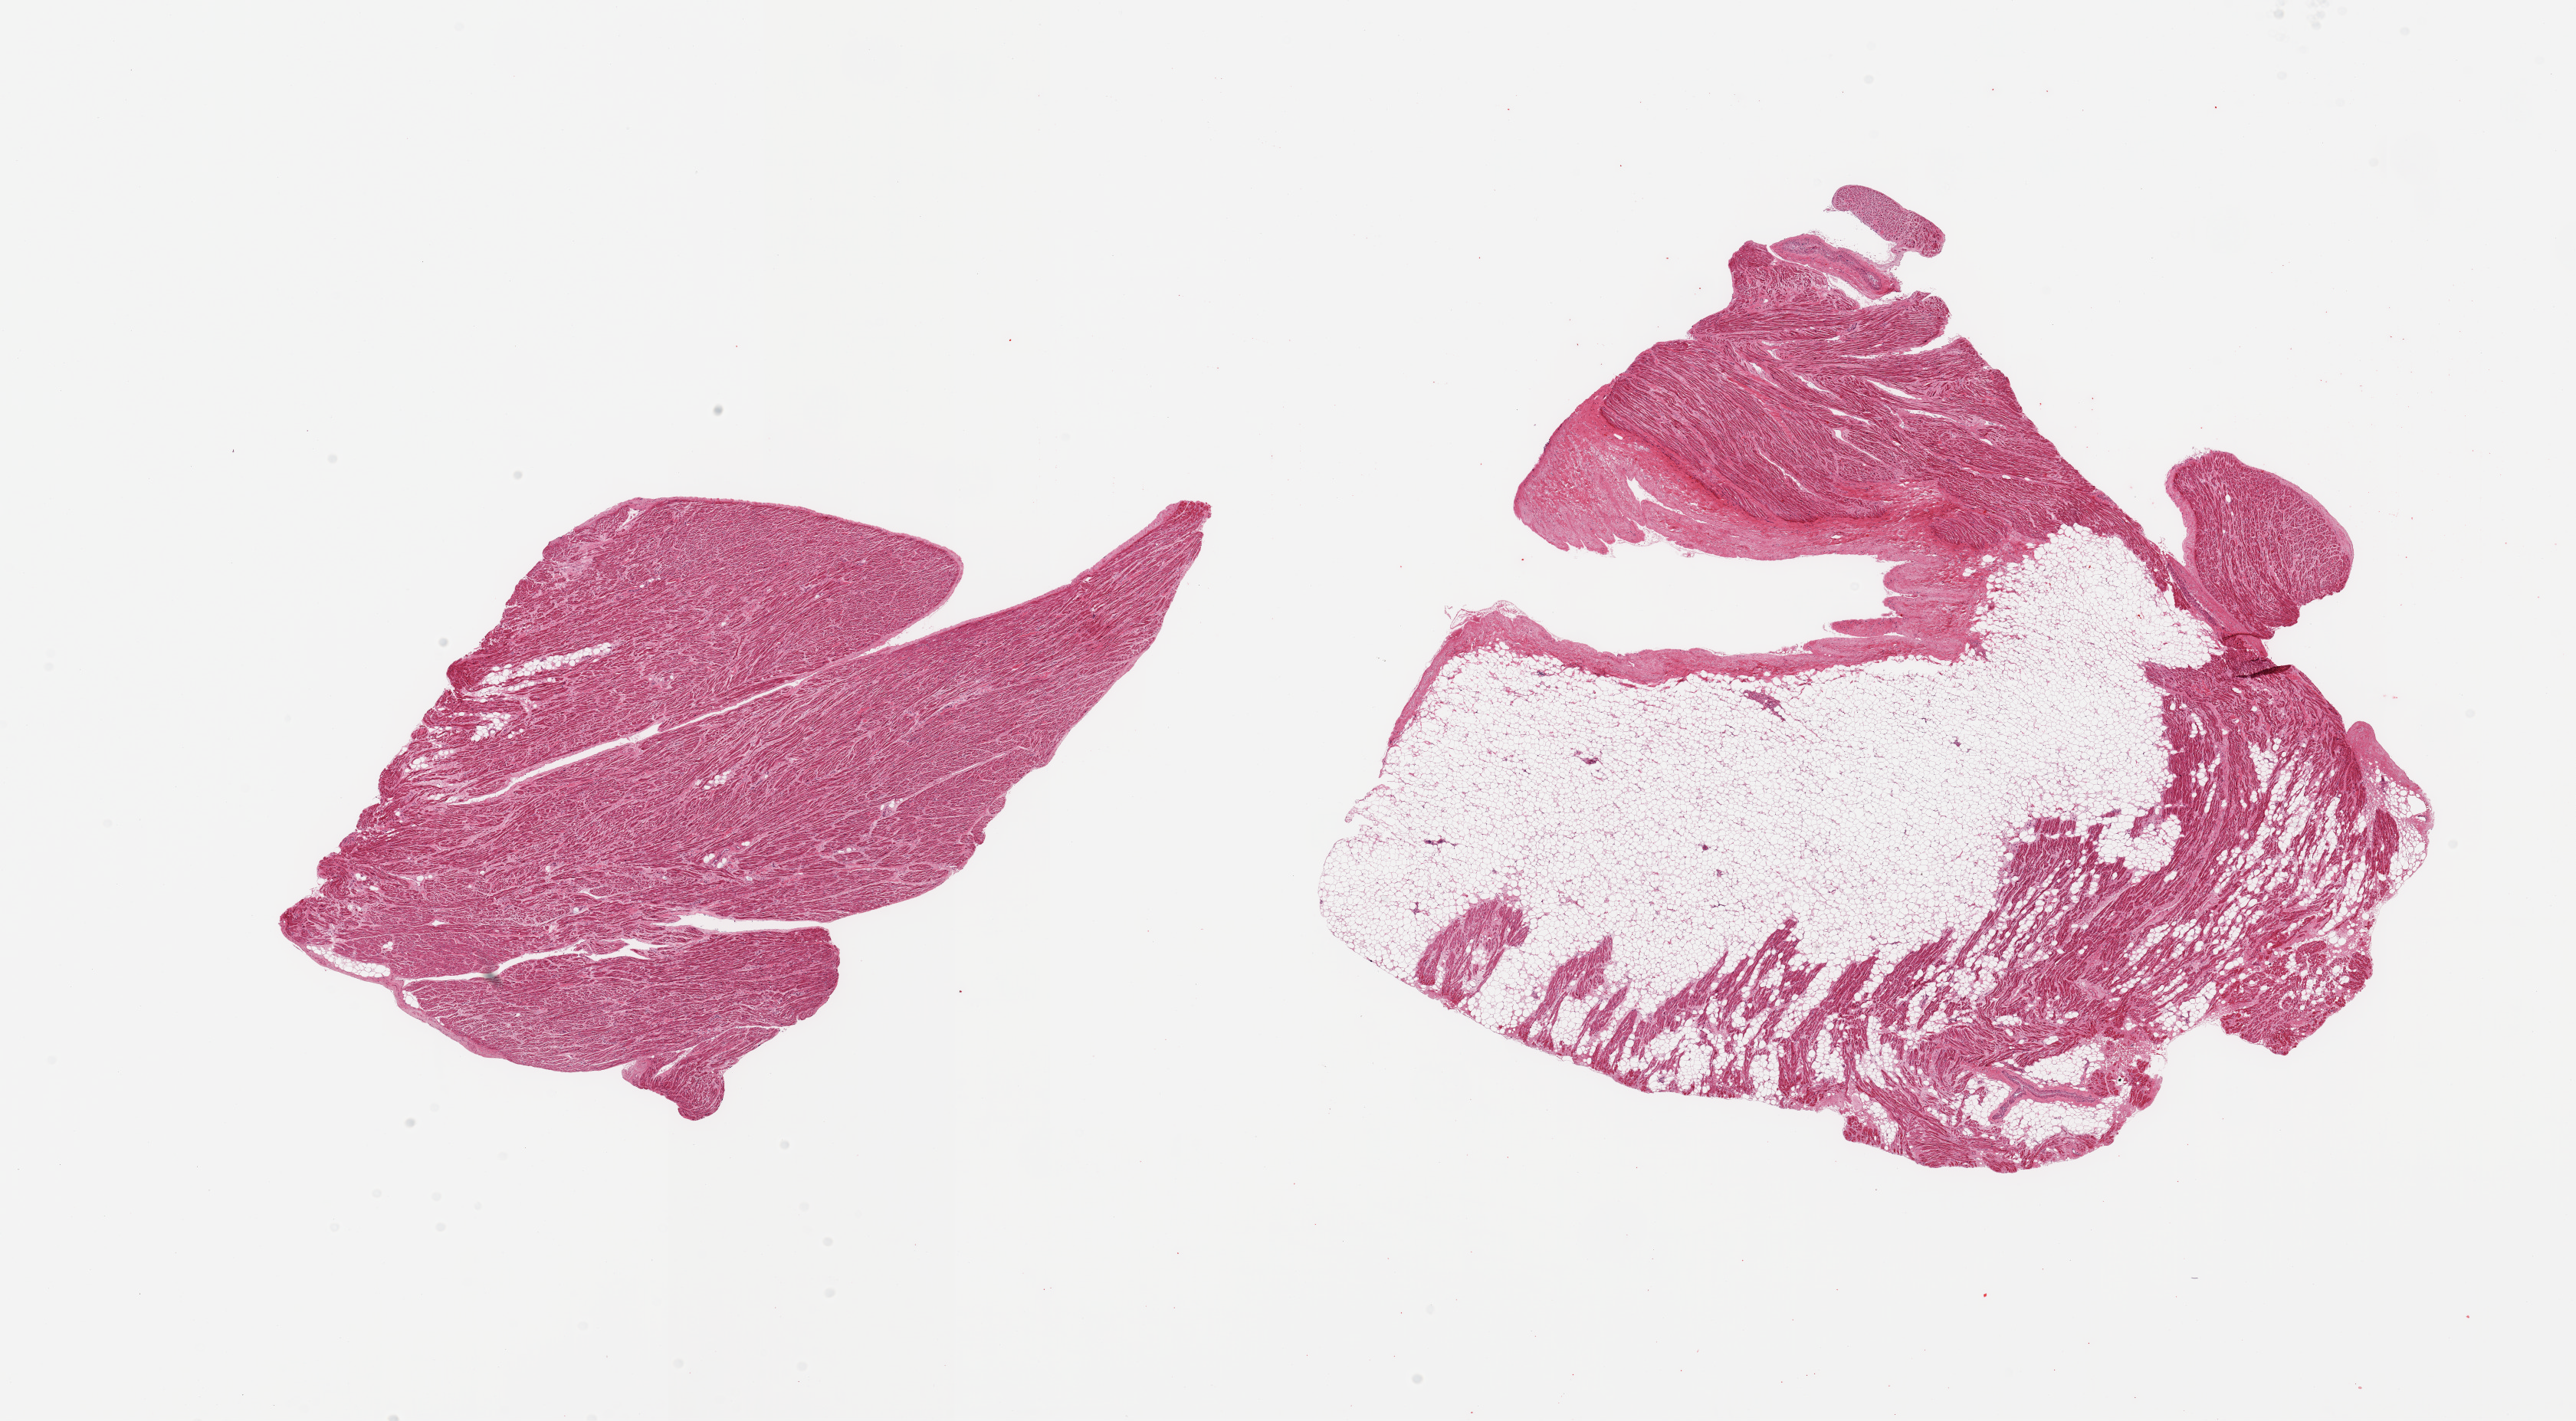
Hematoxylin and eosin (H&E) whole-slide image — whole scanned area (about 26.6 x 14.7 mm, slide scanned at 20x) shown as a low-resolution overview; PAXgene-fixed, paraffin-embedded tissue; section of auricular appendage (target tissue); donor tissue sample. Donor: male.
• reviewer comment on this tissue sample: 2 pieces, no abnormalities